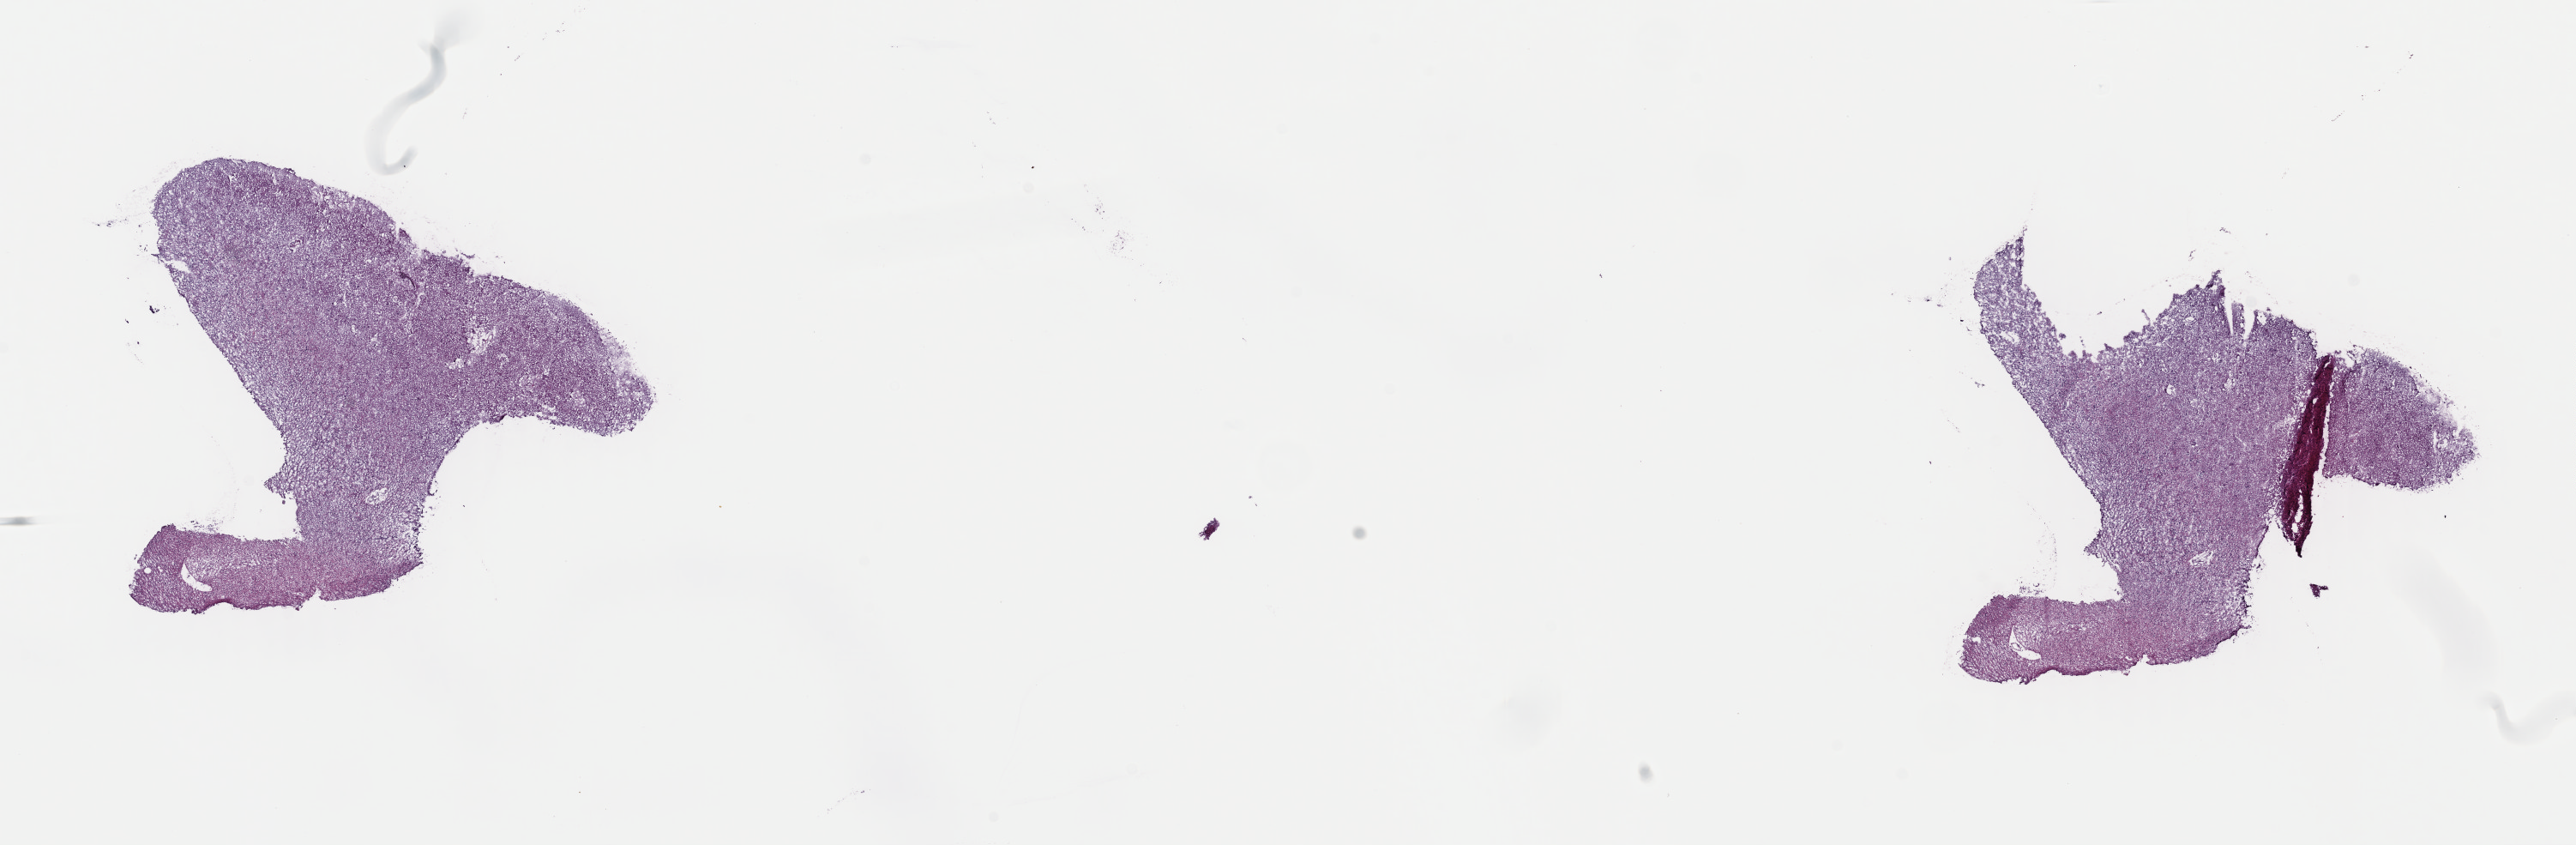
Hematoxylin and eosin (H&E) stained whole-slide image, a low-resolution overview of the entire scanned area, about 23.7 x 7.8 mm (from a 40x scan), frozen section from the top of the tissue portion, brain, primary tumour sample. Male patient; age at initial diagnosis 38 years. Histologic grade: G3 (poorly differentiated). Composition of this section per pathologist review: tumour cells 50%, tumour nuclei 80%, normal cells 10%, stromal cells 40%, necrosis 0%. Infiltration values recorded for this section: lymphocyte infiltration 0%, monocyte infiltration 0%, neutrophil infiltration 0%.
Histologic diagnosis: Mixed glioma. Laterality: right.